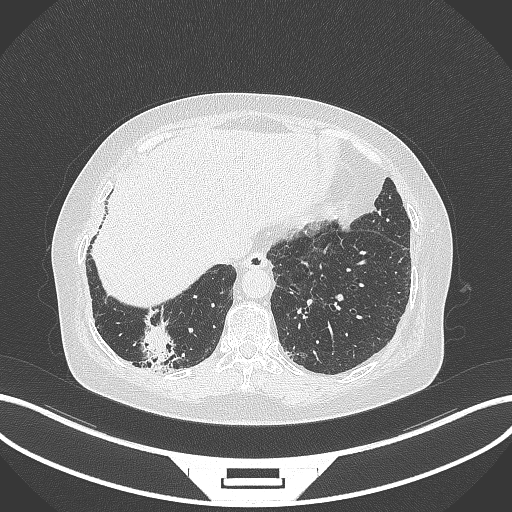
Chest CT, one axial slice. Position 31 of 296 along the scan axis. 120 kVp. Lung window (W 1500 / L -600 HU). 512 × 512 image matrix, field of view 400 × 400 mm. Female patient, age 65 years. From the clinical record (not read from this slice): clinical TNM (as recorded): T2b N1 M0.
Annotated regions visible in this slice (rectangle marked by the reading radiologist):
- lung tumour (recorded histology: adenocarcinoma): box from (x=139, y=317) to (x=178, y=366) px